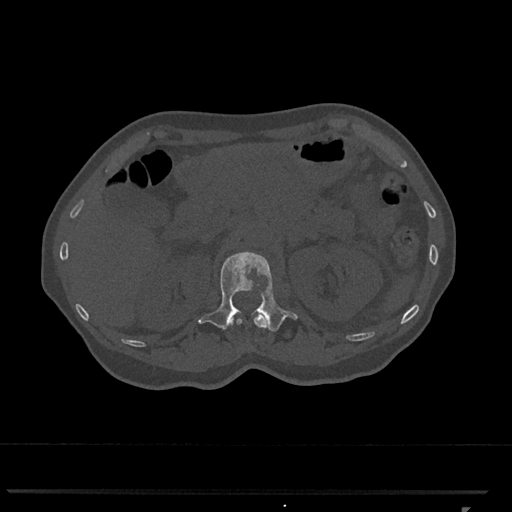
CT including the spine, one axial slice; position 417 of 793 along the scan axis; bone window (W 1800 / L 400 HU); 0.5 mm slice thickness; 512 × 512 image matrix, field of view 380 × 380 mm. Patient: female, 62 years. From the clinical record (not read from this slice): primary cancer: renal.
Outlined on this slice (semi-automatically segmented with operator editing):
- L1 vertebra: bounding box [x1, y1, x2, y2] px = [198, 252, 298, 332]
- T12 vertebra: [229, 313, 267, 328]